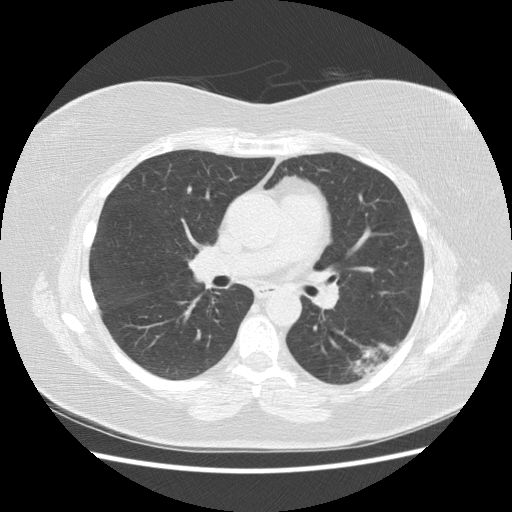
Axial slice from a low-dose chest CT screening exam. Third screening round (two years after baseline). Lung window (W 1500 / L -600 HU). 2.5 mm slice thickness. 120 kVp. 512 × 512 image matrix. Female, age 57 years at enrolment. Current smoker at enrolment.
Expert-annotated lung lesion, bounding box <331,325,412,387> (left, top, right, bottom; pixels). Reader record for this screening exam (exam-level; its link to the box is not recorded): non-calcified nodule or mass ≥4 mm, left lower lobe, 40 × 20 mm, poorly defined margins, mixed attenuation, pre-existing on the prior screen: yes; interval growth: yes. Official screen result: positive, other. Lung cancer was diagnosed 55 days after this screen: squamous cell carcinoma, NOS, left lower lobe, poorly differentiated (G3), stage IB (AJCC 6th edition), 40 mm at pathology.